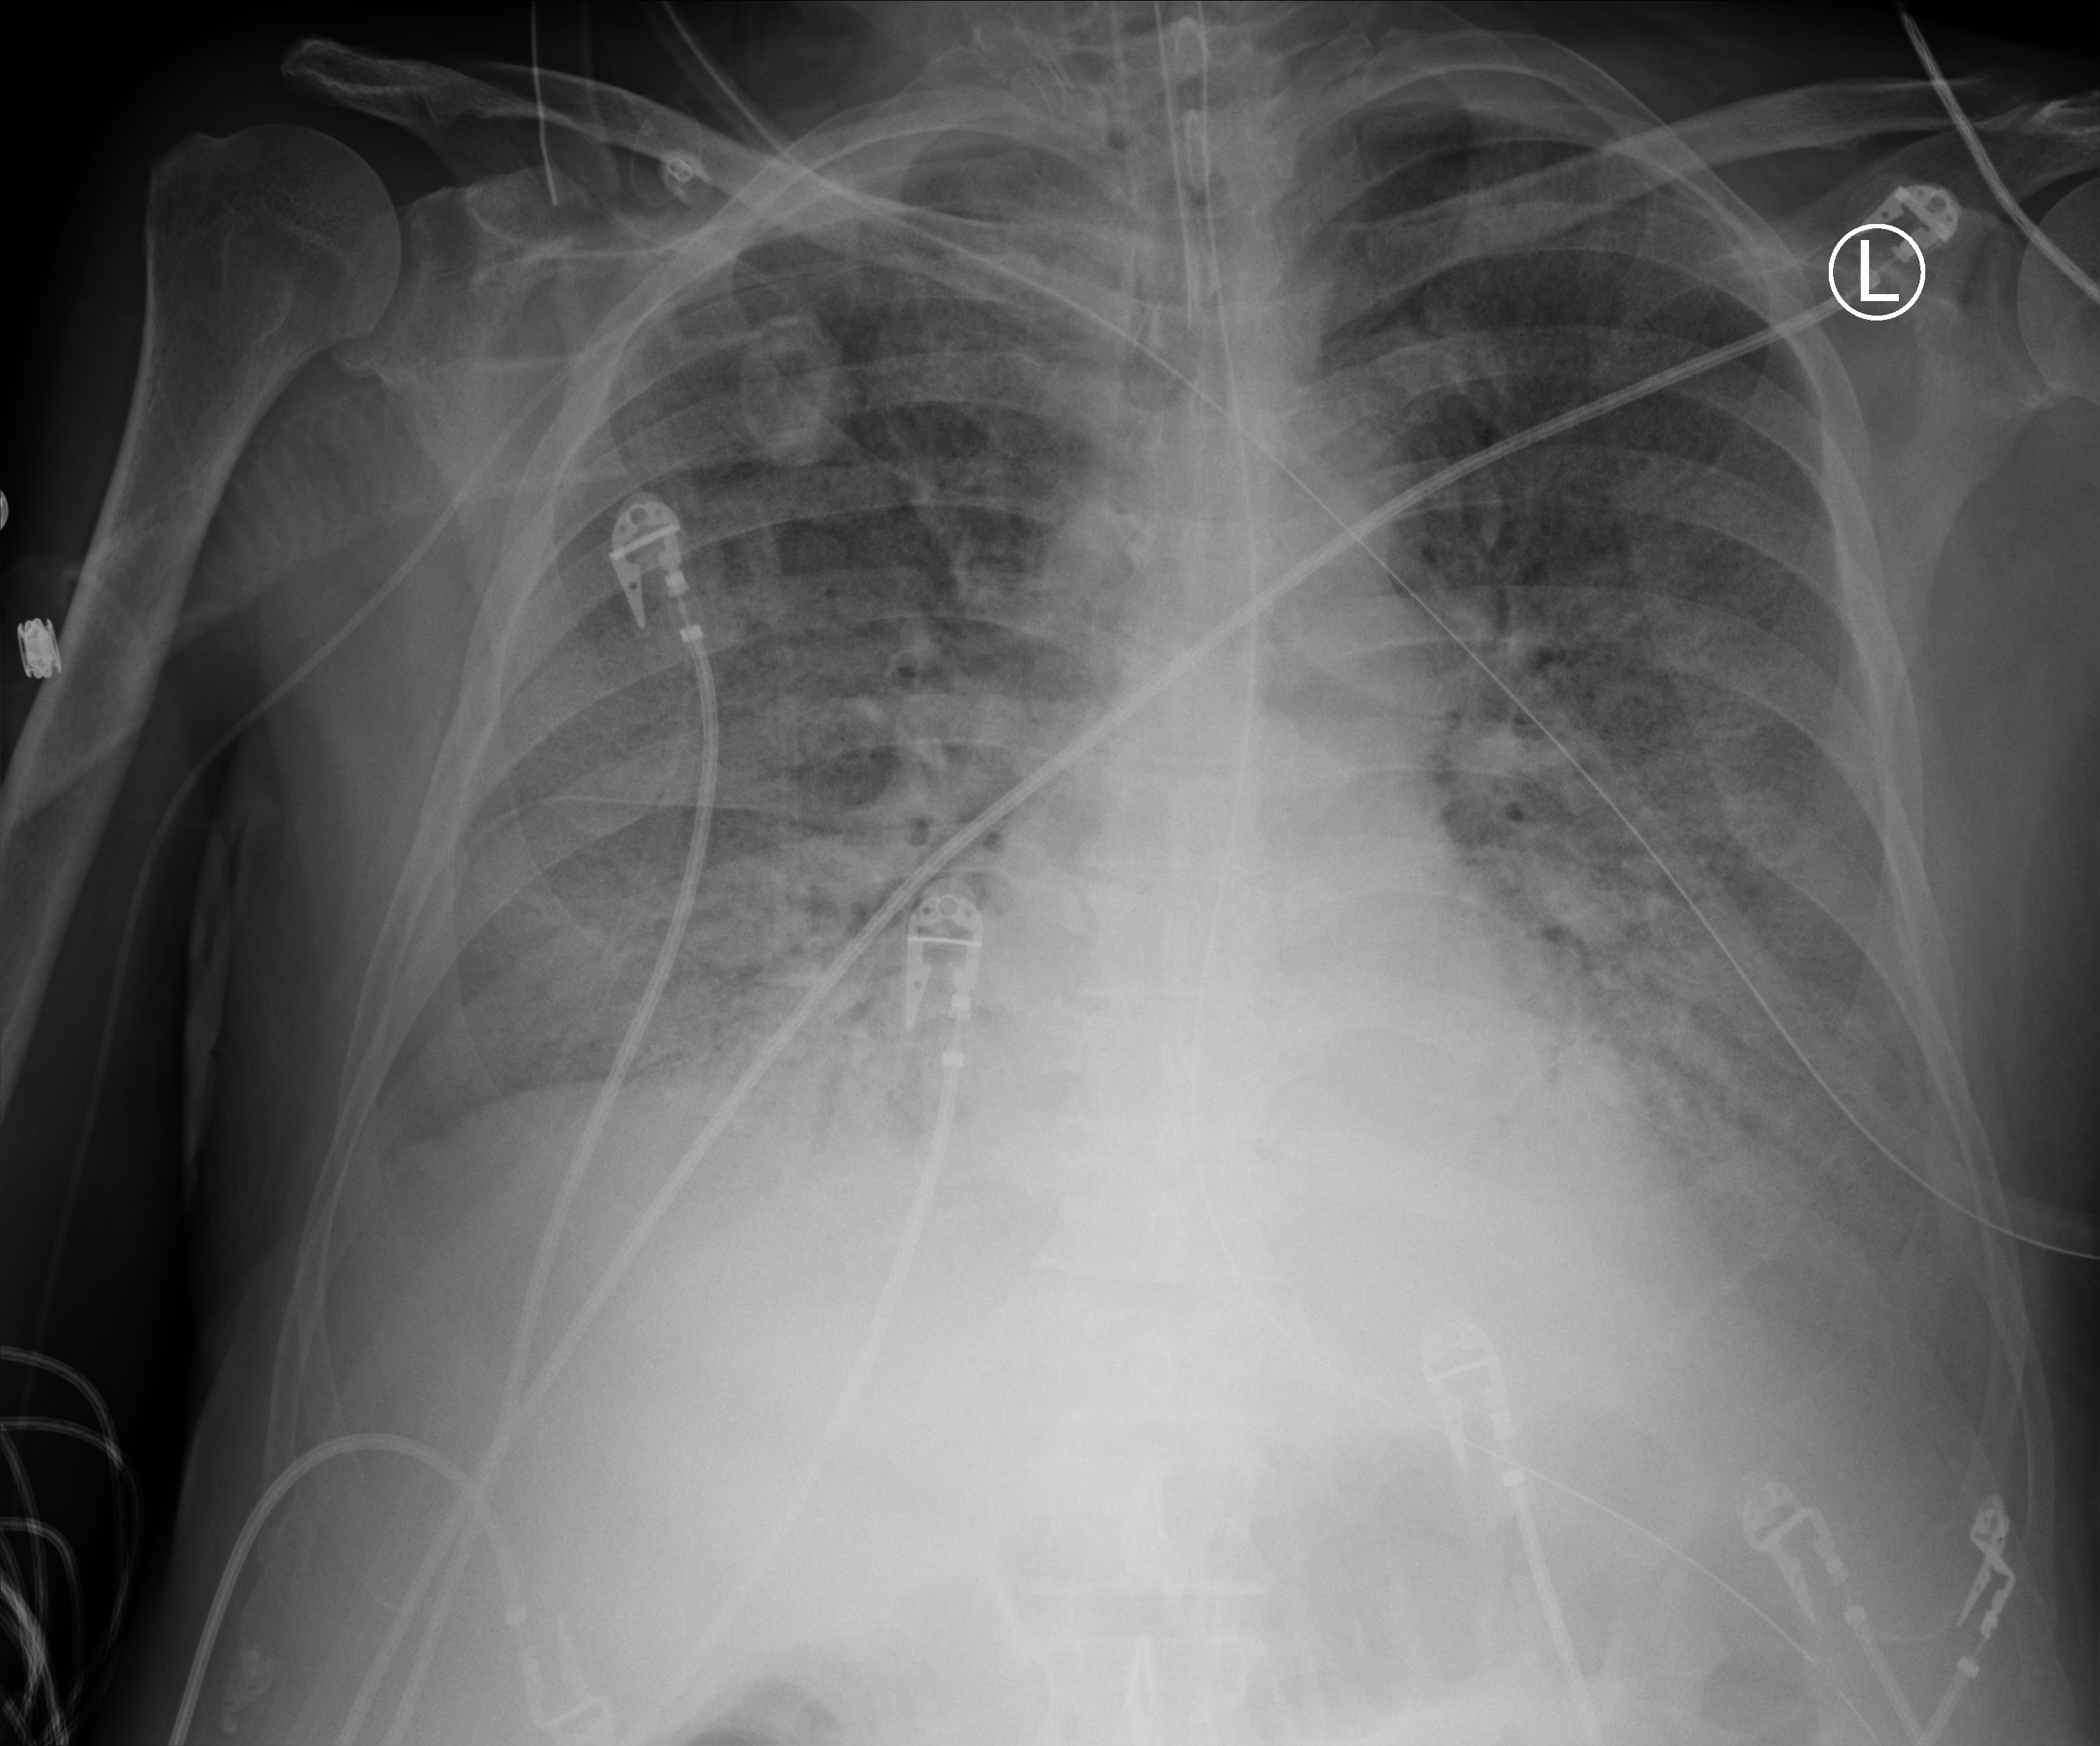
Portable chest radiograph, anteroposterior (AP) projection. Male patient hospitalised with COVID-19, age 60–74 years.
Hospital-stay facts (about this admission, not read from this image; timing relative to this image not recorded): smoking status (admission record): former.